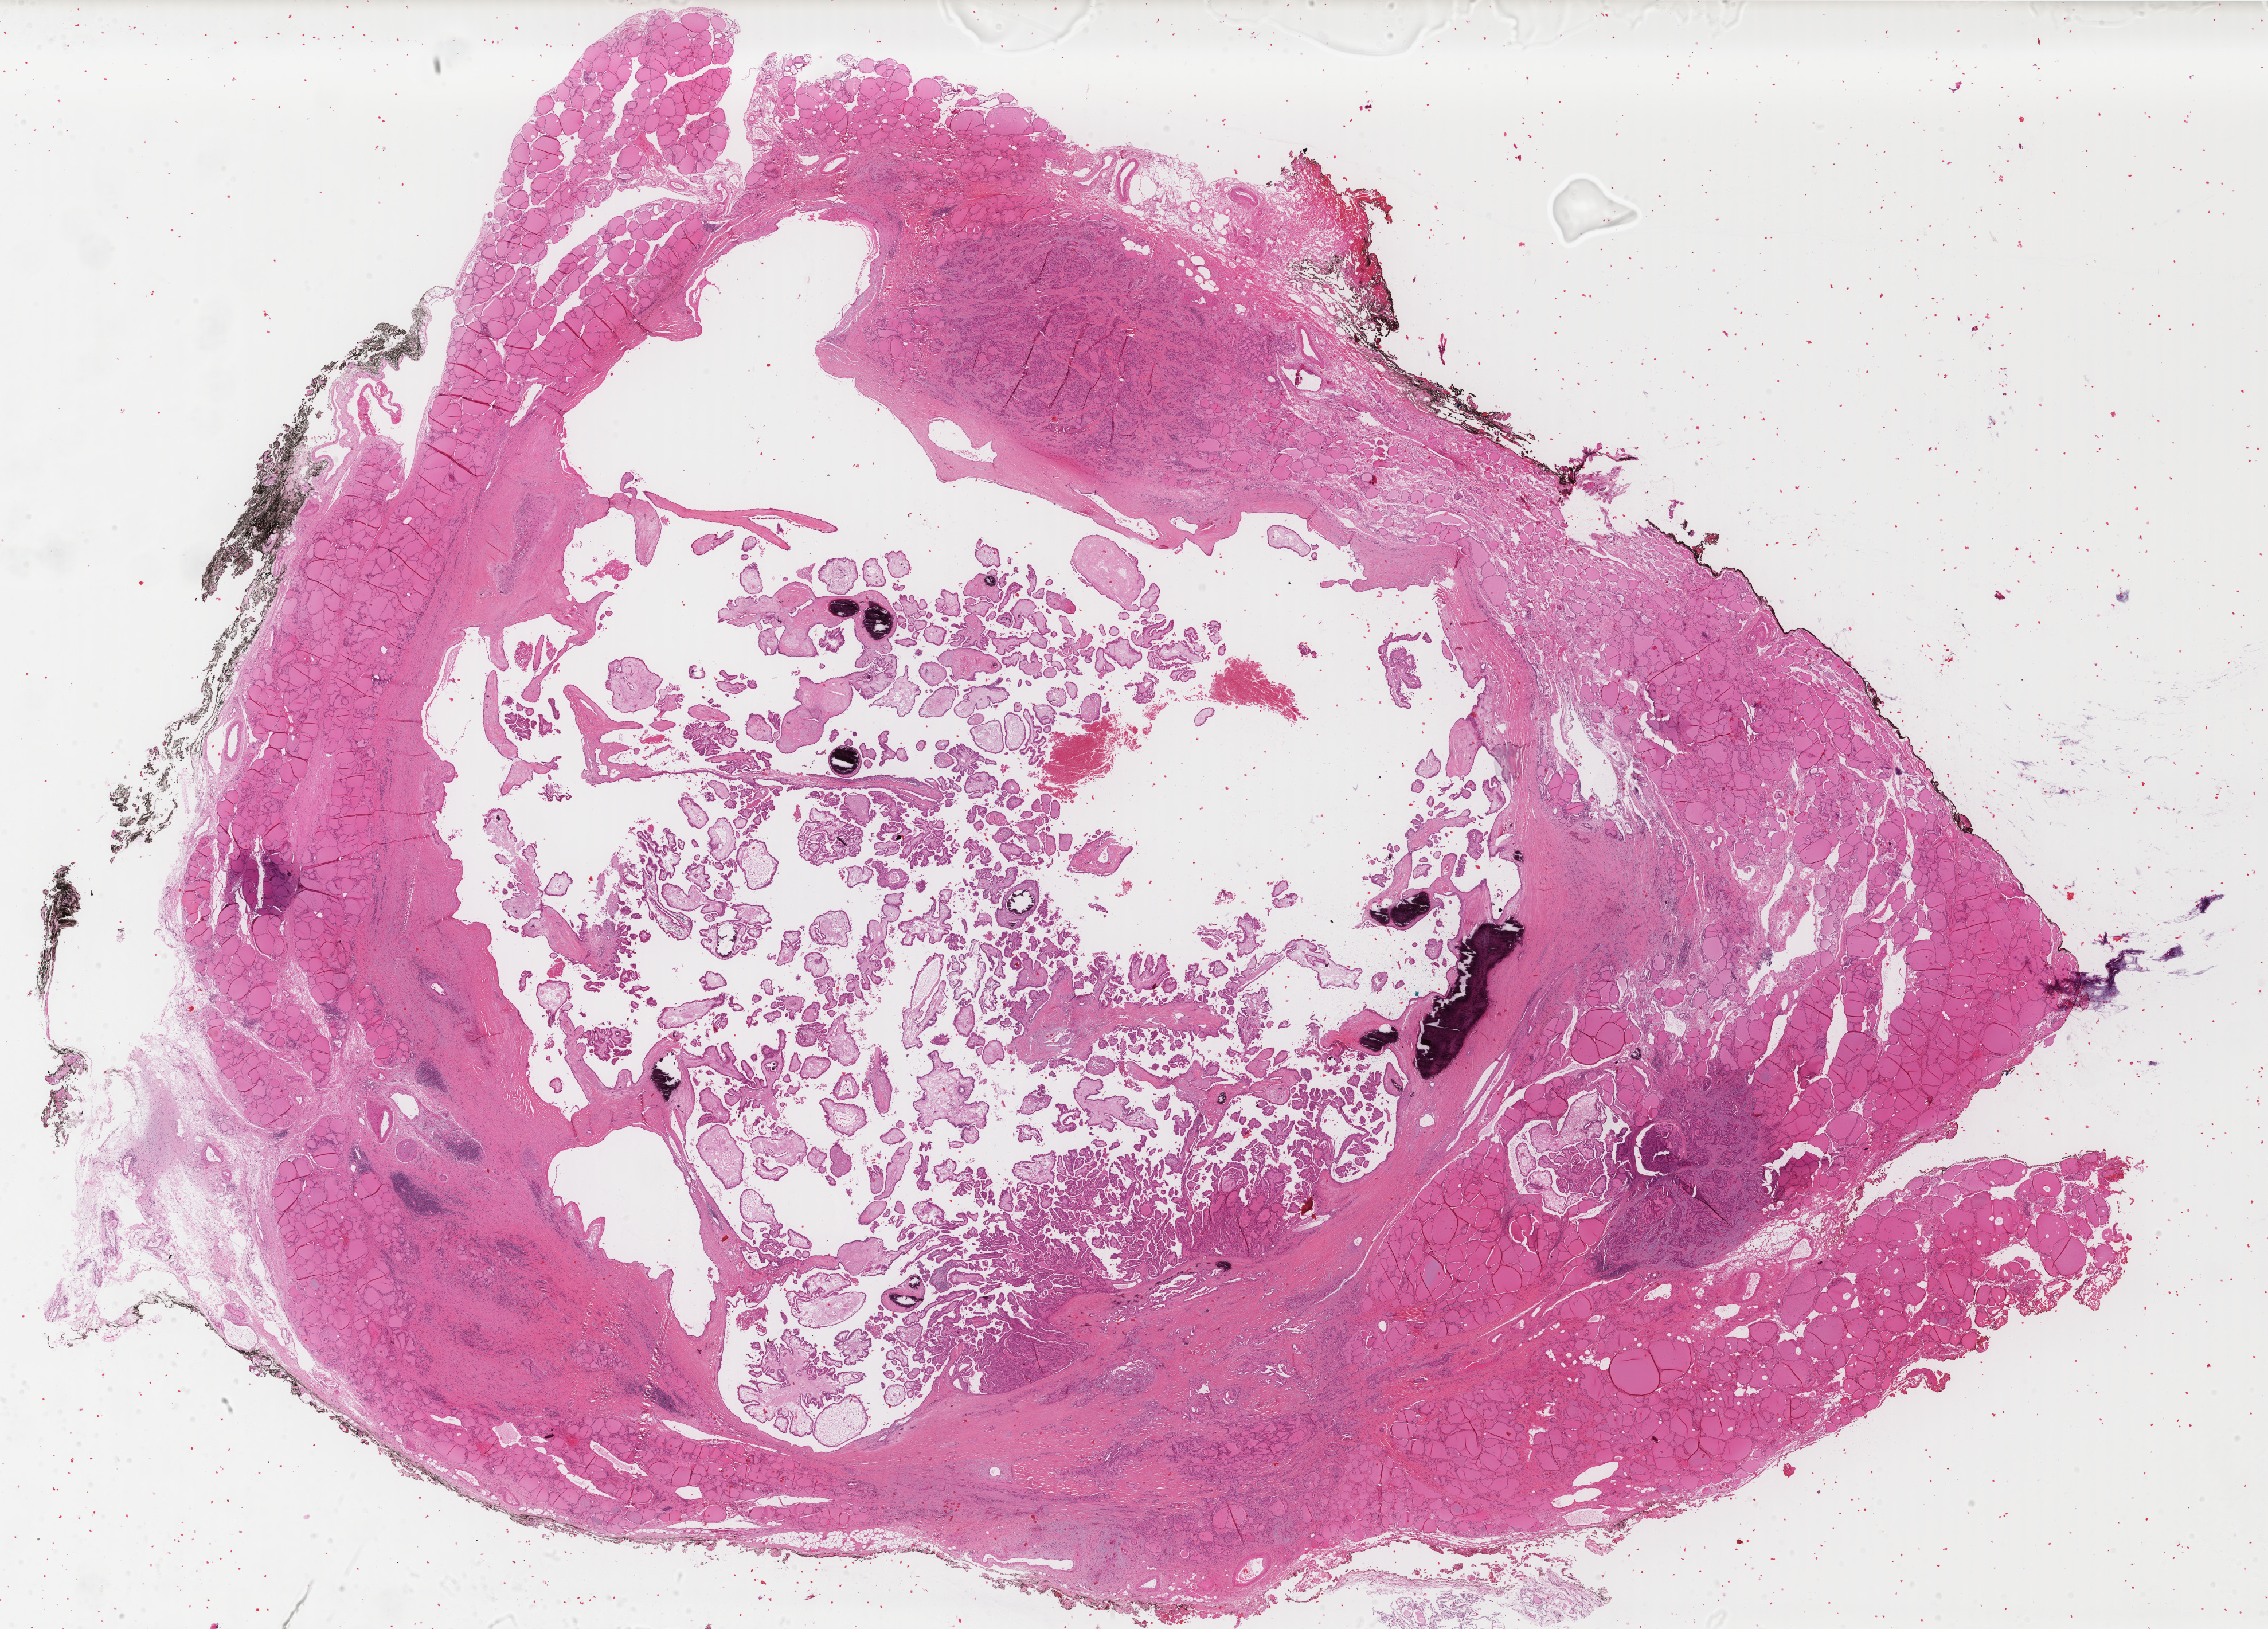
H&E whole-slide image — a low-resolution overview of the entire scanned area, about 31.4 x 22.6 mm. Formalin-fixed paraffin-embedded (FFPE) diagnostic section. Sample: primary tumour, thyroid. Female, age 54 years at initial diagnosis.
Diagnosis: Papillary adenocarcinoma, NOS (thyroid gland). AJCC pathologic stage: III (7th edition). Lymph nodes positive (case pathology): 6 of 9 examined. Laterality: bilateral.